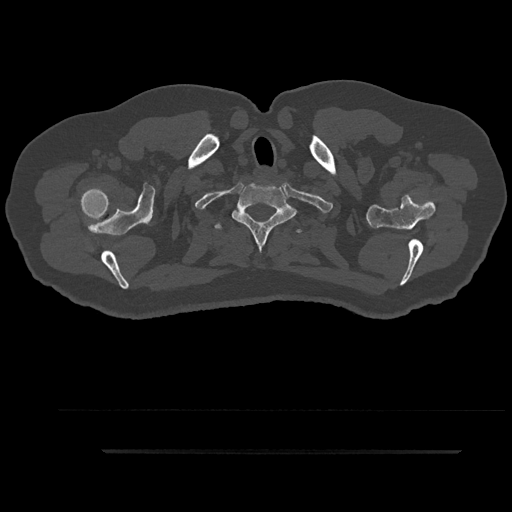
CT including the spine, one axial slice. Slice 794 of 797 in the series (ordered by position). Reconstruction kernel Br40s/3. 120 kVp. Bone window (W 1800 / L 400 HU). 0.5 mm slice thickness. 512 × 512 image matrix, field of view 432 × 432 mm. Male patient, age 63 years. Case-level facts recorded for this patient, not image findings: primary cancer: renal; vertebrae with lytic lesions (as recorded): T8.
Annotated regions visible in this slice (semi-automatically segmented with operator editing):
- T1 vertebra: box from (x=232, y=185) to (x=299, y=251) px
- T2 vertebra: (x=214, y=223)–(x=303, y=235)